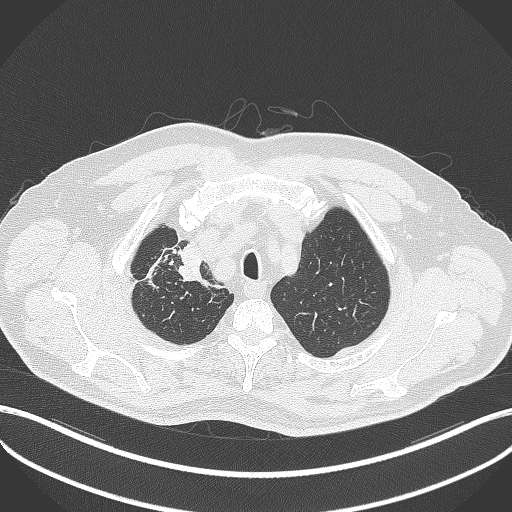
Chest CT, one axial slice. Slice 331 of 411 in the series (ordered by position). Reconstruction kernel B70f. 120 kVp. Lung window (W 1500 / L -600 HU). 512 × 512 image matrix. Patient: male, 60 years. Case-level facts recorded for this patient, not image findings: clinical TNM (as recorded): T1b N1 M0.
Outlined on this slice (bounding box drawn by a radiologist):
- lung tumour (recorded histology: squamous cell carcinoma): box from (x=176, y=241) to (x=224, y=286) px